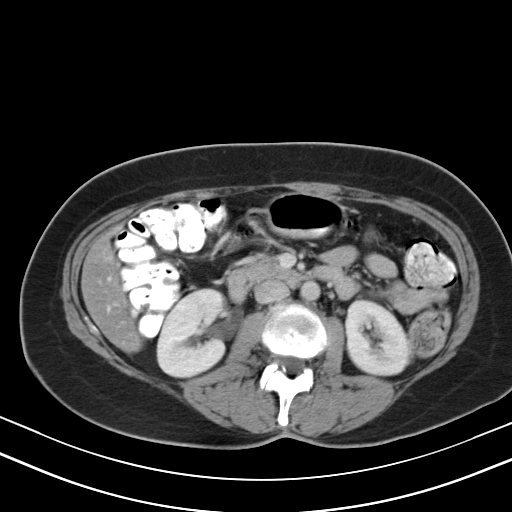
Contrast-enhanced abdominal CT, one axial slice. Slice 18 of 47 in the series (ordered by position). Reconstruction kernel B40s. 130 kVp. Soft-tissue window (W 400 / L 40 HU). 5 mm slice thickness. 512 × 512 image matrix. Female patient. Case-level facts recorded for this patient, not image findings: diagnosis: colorectal cancer liver metastases, imaged before liver resection.
Structures marked on this image (expert manual segmentation):
- liver: bounding box [x1, y1, x2, y2] px = [83, 237, 140, 351]
- planned liver remnant (the part of the liver to remain after resection): [83, 237, 140, 351]